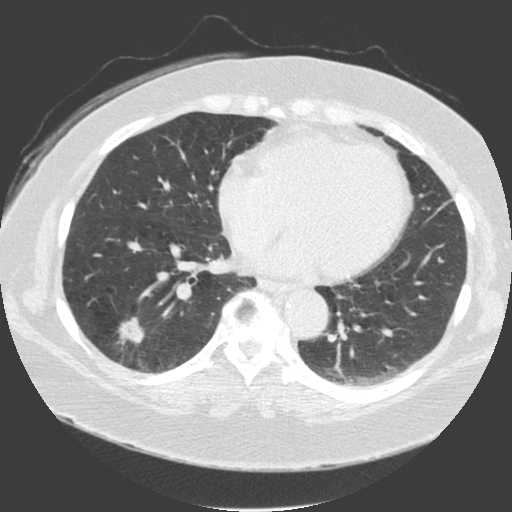
Axial slice from a low-dose chest CT screening exam. Third annual screen. Lung window (W 1500 / L -600 HU). 2 mm slice thickness. 120 kVp. Slice 103 of 175 in the series. 512 × 512 image matrix, field of view 370 × 370 mm. Female participant, aged 56 years at enrolment. Current smoker at enrolment.
- Lesion marked by an expert reader, bounding box (x1, y1, x2, y2) in pixels: (98, 301, 155, 356).
- The screening reader recorded 4 non-calcified nodules or masses ≥4 mm on this exam (left lower lobe, right lower lobe, right lower lobe, right lower lobe); which of them this box marks is not recorded.
- Later outcome: lung cancer diagnosed 20 days after this screen — adenosquamous carcinoma, right lower lobe, poorly differentiated (G3), stage IA (AJCC 6th edition), 25 mm at pathology.